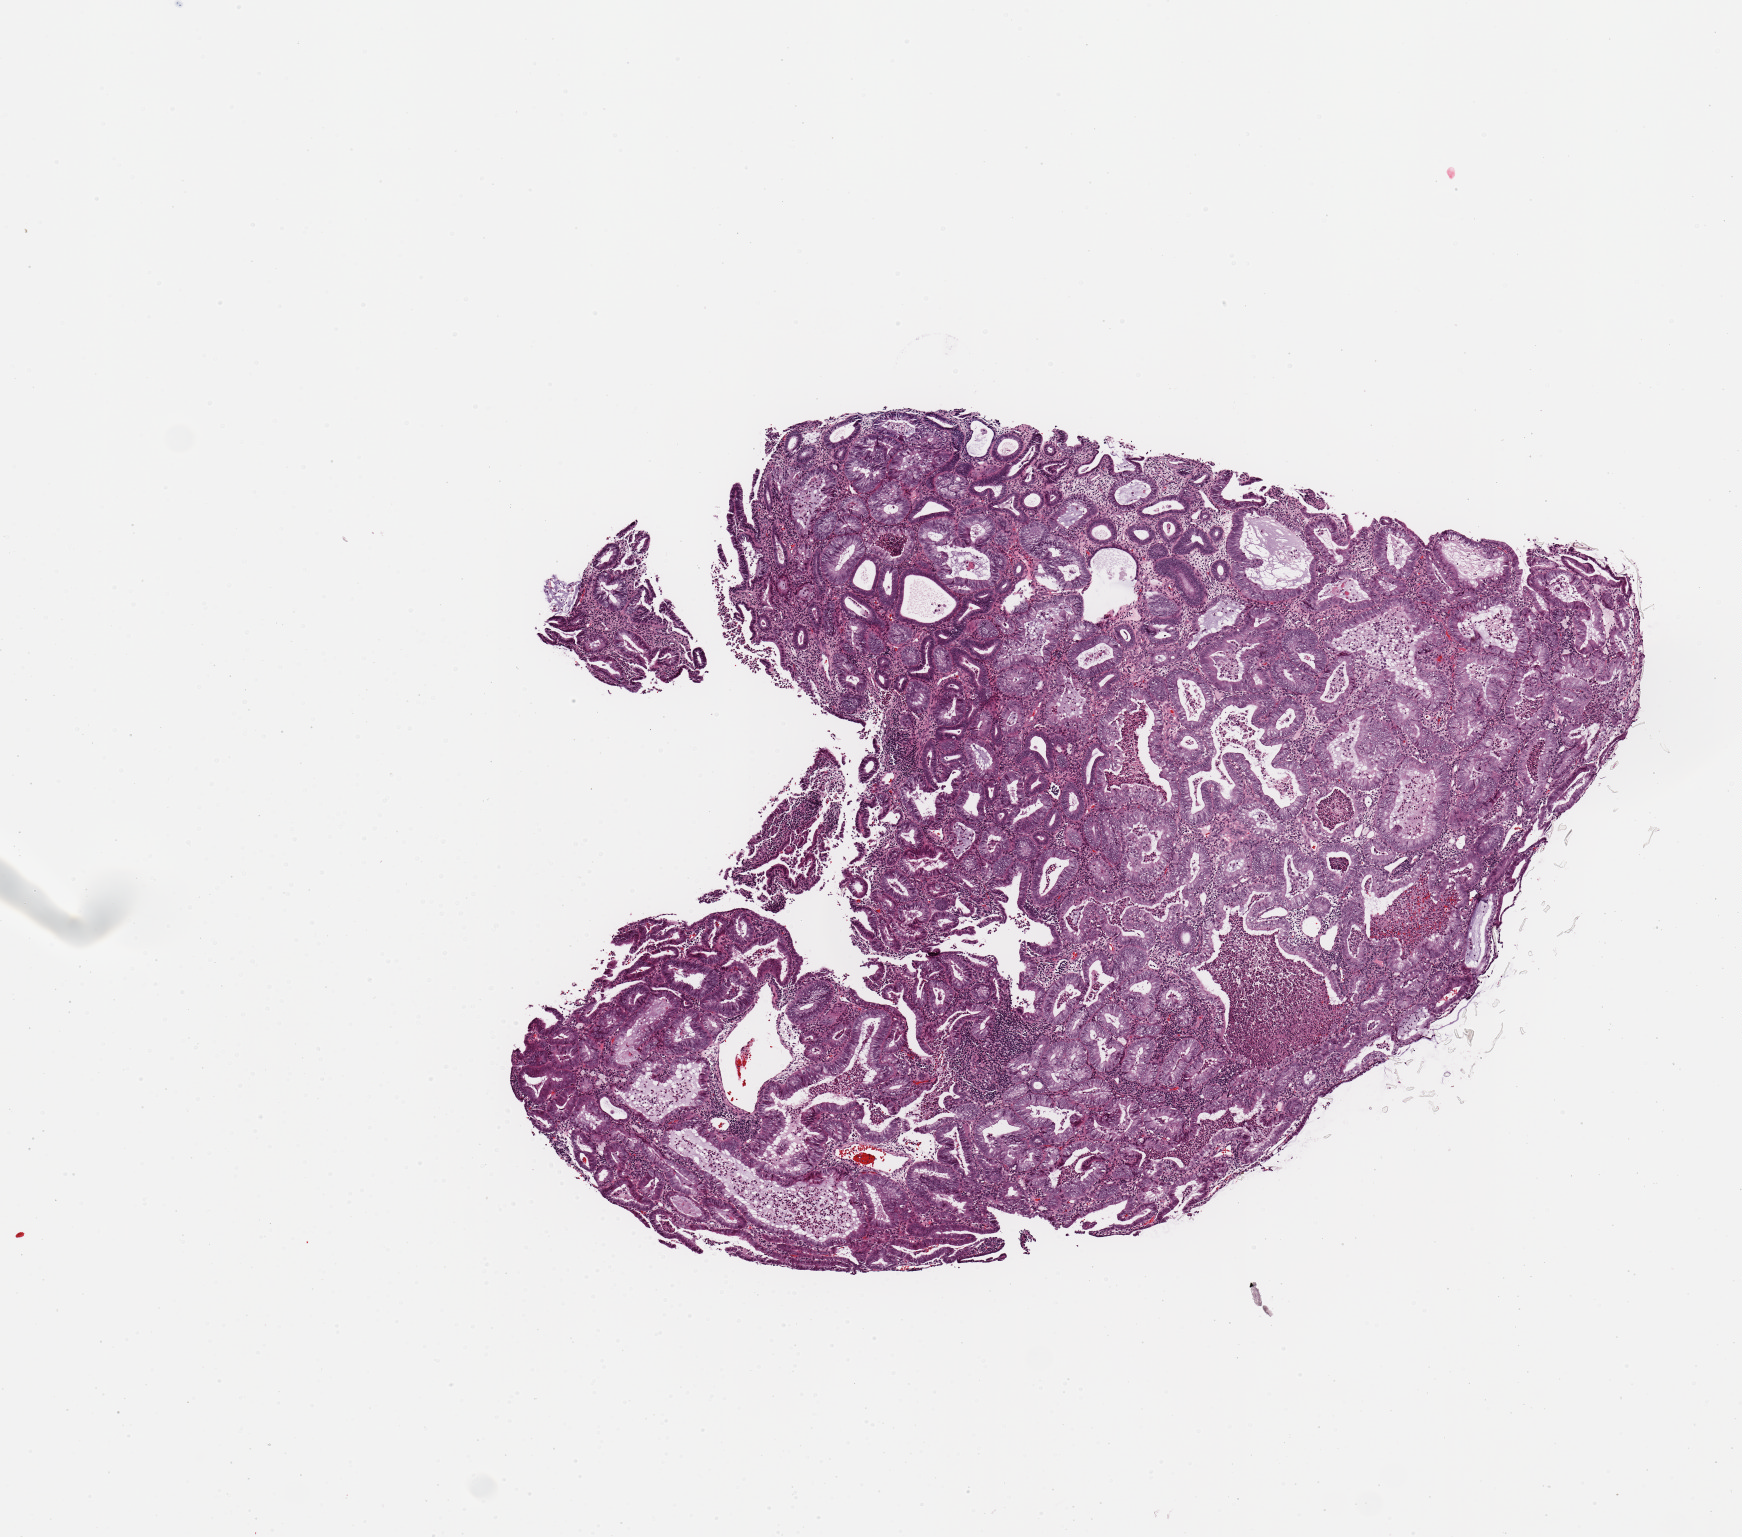
Whole-slide histology image, H&E-stained, shown as a low-resolution overview of the whole scanned area (about 6.9 x 6.1 mm, acquisition: 20x scan); tumour tissue sample, sampled site: uterus. Female, 54 y/o. Histologic grade: G2 (moderately differentiated). Slide review estimates, as recorded: tumour nuclei 90%, necrosis 2%.
Diagnosis: Endometrioid adenocarcinoma, NOS. AJCC pathologic stage: I.